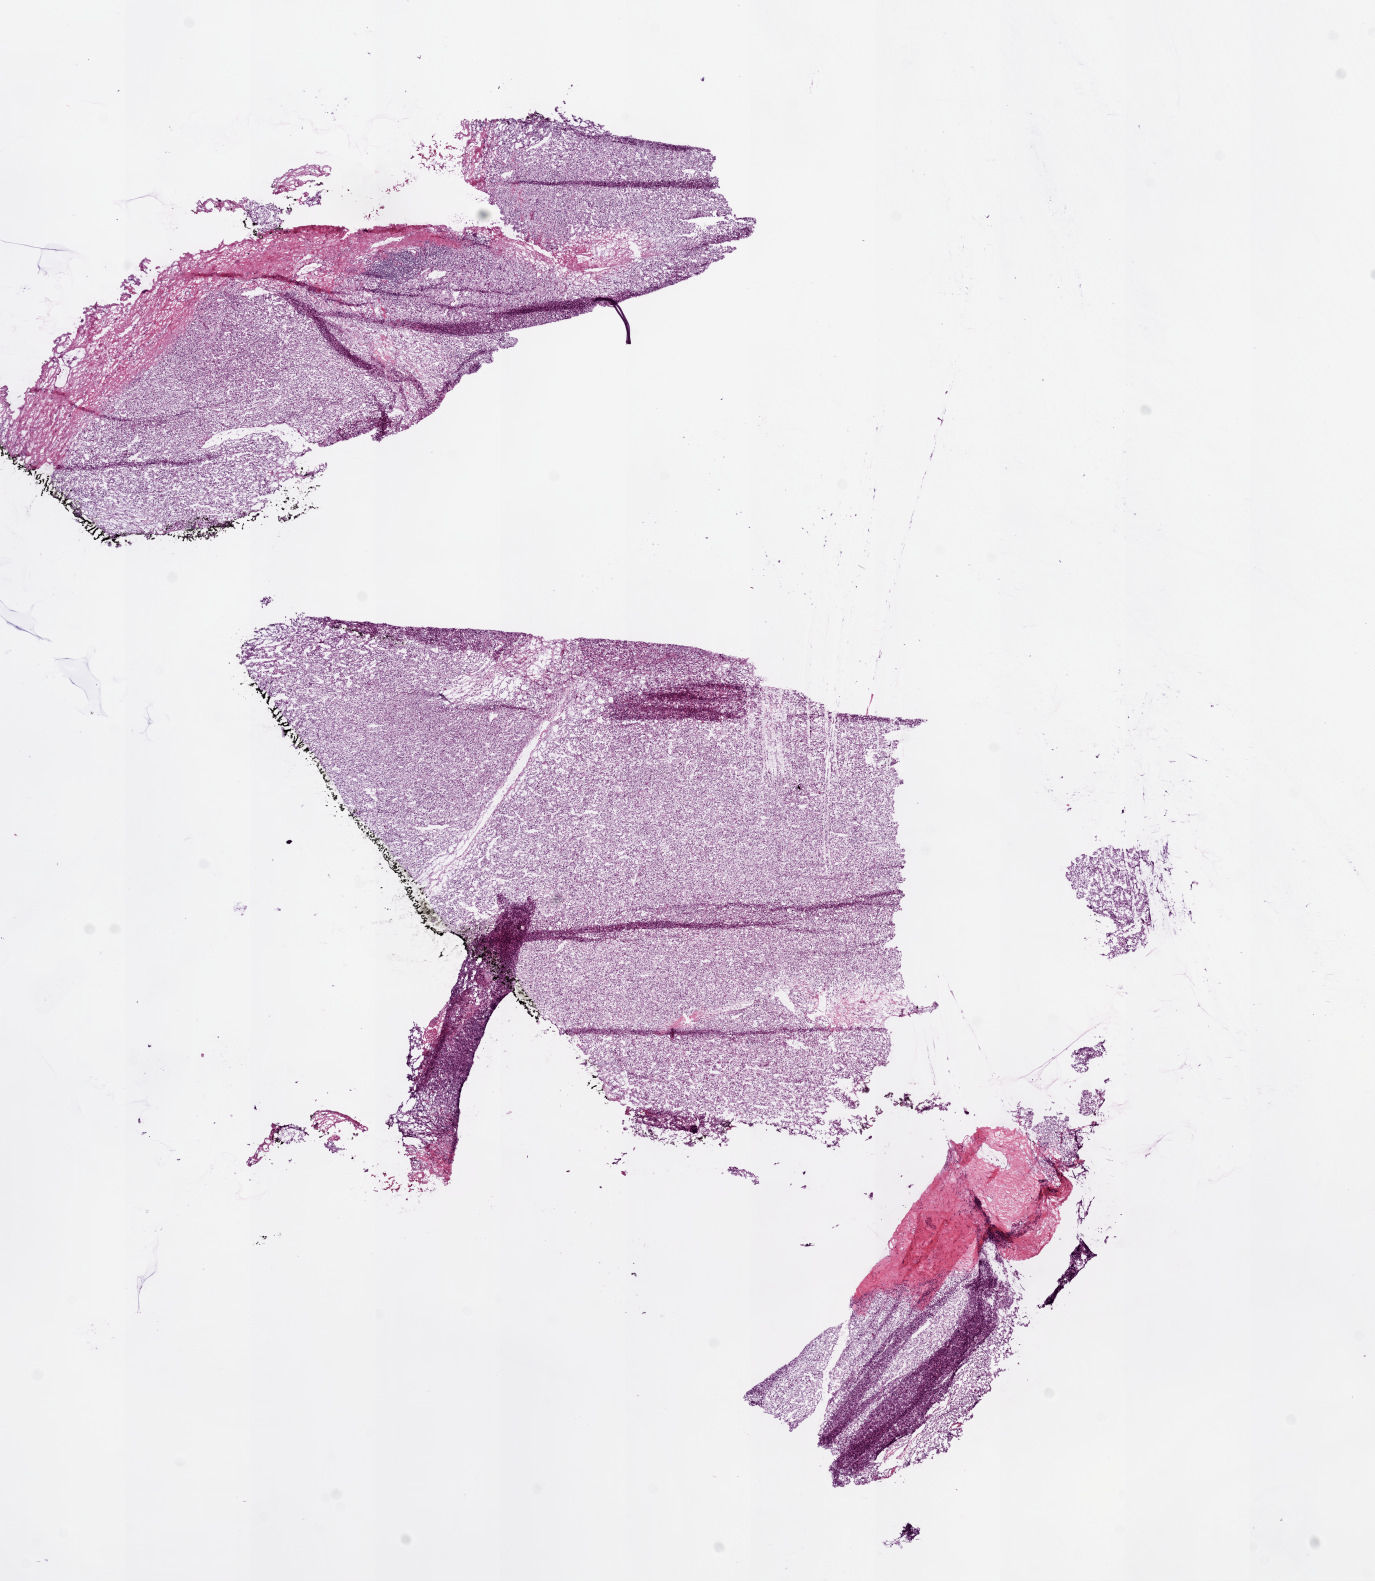
Whole-slide histology image, H&E-stained, low-resolution overview of the scanned area, about 11.0 x 12.7 mm (acquisition: 20x scan), frozen section, kidney, primary tumour sample. Male patient; age at initial diagnosis 72 years. Histologic grade: G3 (poorly differentiated). Slide review estimates, as recorded: tumour cells 90%, tumour nuclei 80%, normal cells 0%, stromal cells 10%, necrosis 0%.
- histologic diagnosis: Clear cell adenocarcinoma, NOS
- AJCC pathologic stage: I